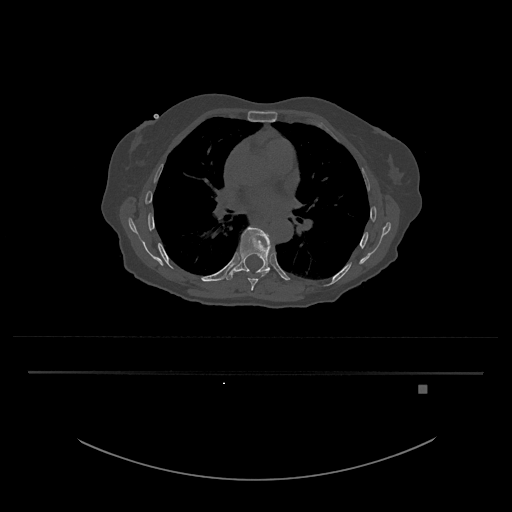
CT including the spine, one axial slice; position 779 of 797 along the scan axis; bone window (W 1800 / L 400 HU); 0.5 mm slice thickness; 512 × 512 image matrix, field of view 500 × 500 mm. Patient: female, 57 years. From the clinical record (not read from this slice): primary cancer: cervical.
Outlined on this slice (semi-automatically segmented with operator editing):
- T8 vertebra: bounding box [x1, y1, x2, y2] px = [242, 270, 266, 291]
- T9 vertebra: [224, 227, 274, 281]